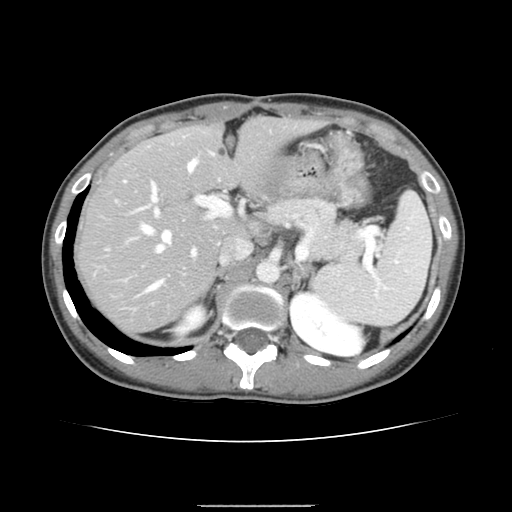
Contrast-enhanced abdominal CT, one axial slice. Slice 98 of 150 in the series (ordered by position). 120 kVp. Intravenous contrast given. Soft-tissue window (W 400 / L 40 HU). 512 × 512 image matrix. Female patient, age 32 years. From the clinical record (not read from this slice): diagnosis: colorectal cancer liver metastases, imaged before liver resection; multiple liver metastases: yes.
Annotated regions visible in this slice (manually delineated by an expert):
- hepatic veins: bounding box (x1, y1, x2, y2) in pixels: (142, 159, 198, 290)
- liver: (79, 119, 312, 332)
- planned liver remnant (the part of the liver to remain after resection): (78, 118, 313, 281)
- portal vein (with intrahepatic branches): (124, 158, 229, 256)